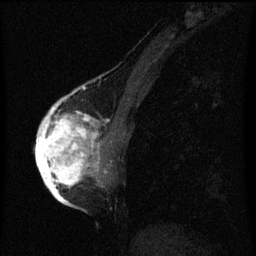
Breast MRI (dynamic contrast-enhanced), one sagittal slice; position 26 of 60 along the scan axis; dynamic contrast-enhanced series, image 2 of 3 at this slice position (ordered by acquisition); 1.5 T; TE 4.2 ms, TR 8 ms; 2 mm slice thickness; 256 × 256 image matrix, field of view 180 × 180 mm. Female patient, age 56 years.
Annotated regions visible in this slice (semi-automatic segmentation, software-assisted and operator-edited):
- analysis volume of interest (the breast-tissue region the enhancement analysis was run in; not a lesion): bounding box <42,110,105,193> (left, top, right, bottom; pixels)
- tumour enhancement mask (voxels above the 70 % enhancement threshold inside the analysis volume of interest): <42,110,99,193>